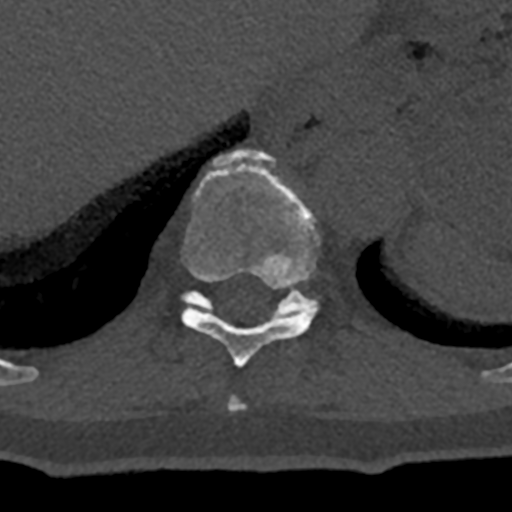
CT including the spine, one axial slice; position 591 of 797 along the scan axis; reconstruction kernel Br40s/3; bone window (W 1800 / L 400 HU); 512 × 512 image matrix. Patient: male, 74 years. Case-level facts recorded for this patient, not image findings: primary cancer: renal; vertebrae with lytic lesions (as recorded): T10, L1, L2, L3, L4, L5.
Annotated regions visible in this slice (semi-automatically segmented with operator editing):
- T10 vertebra: bounding box <181,150,320,368> (left, top, right, bottom; pixels)
- T11 vertebra: <182,281,317,320>
- T9 vertebra: <227,396,244,411>